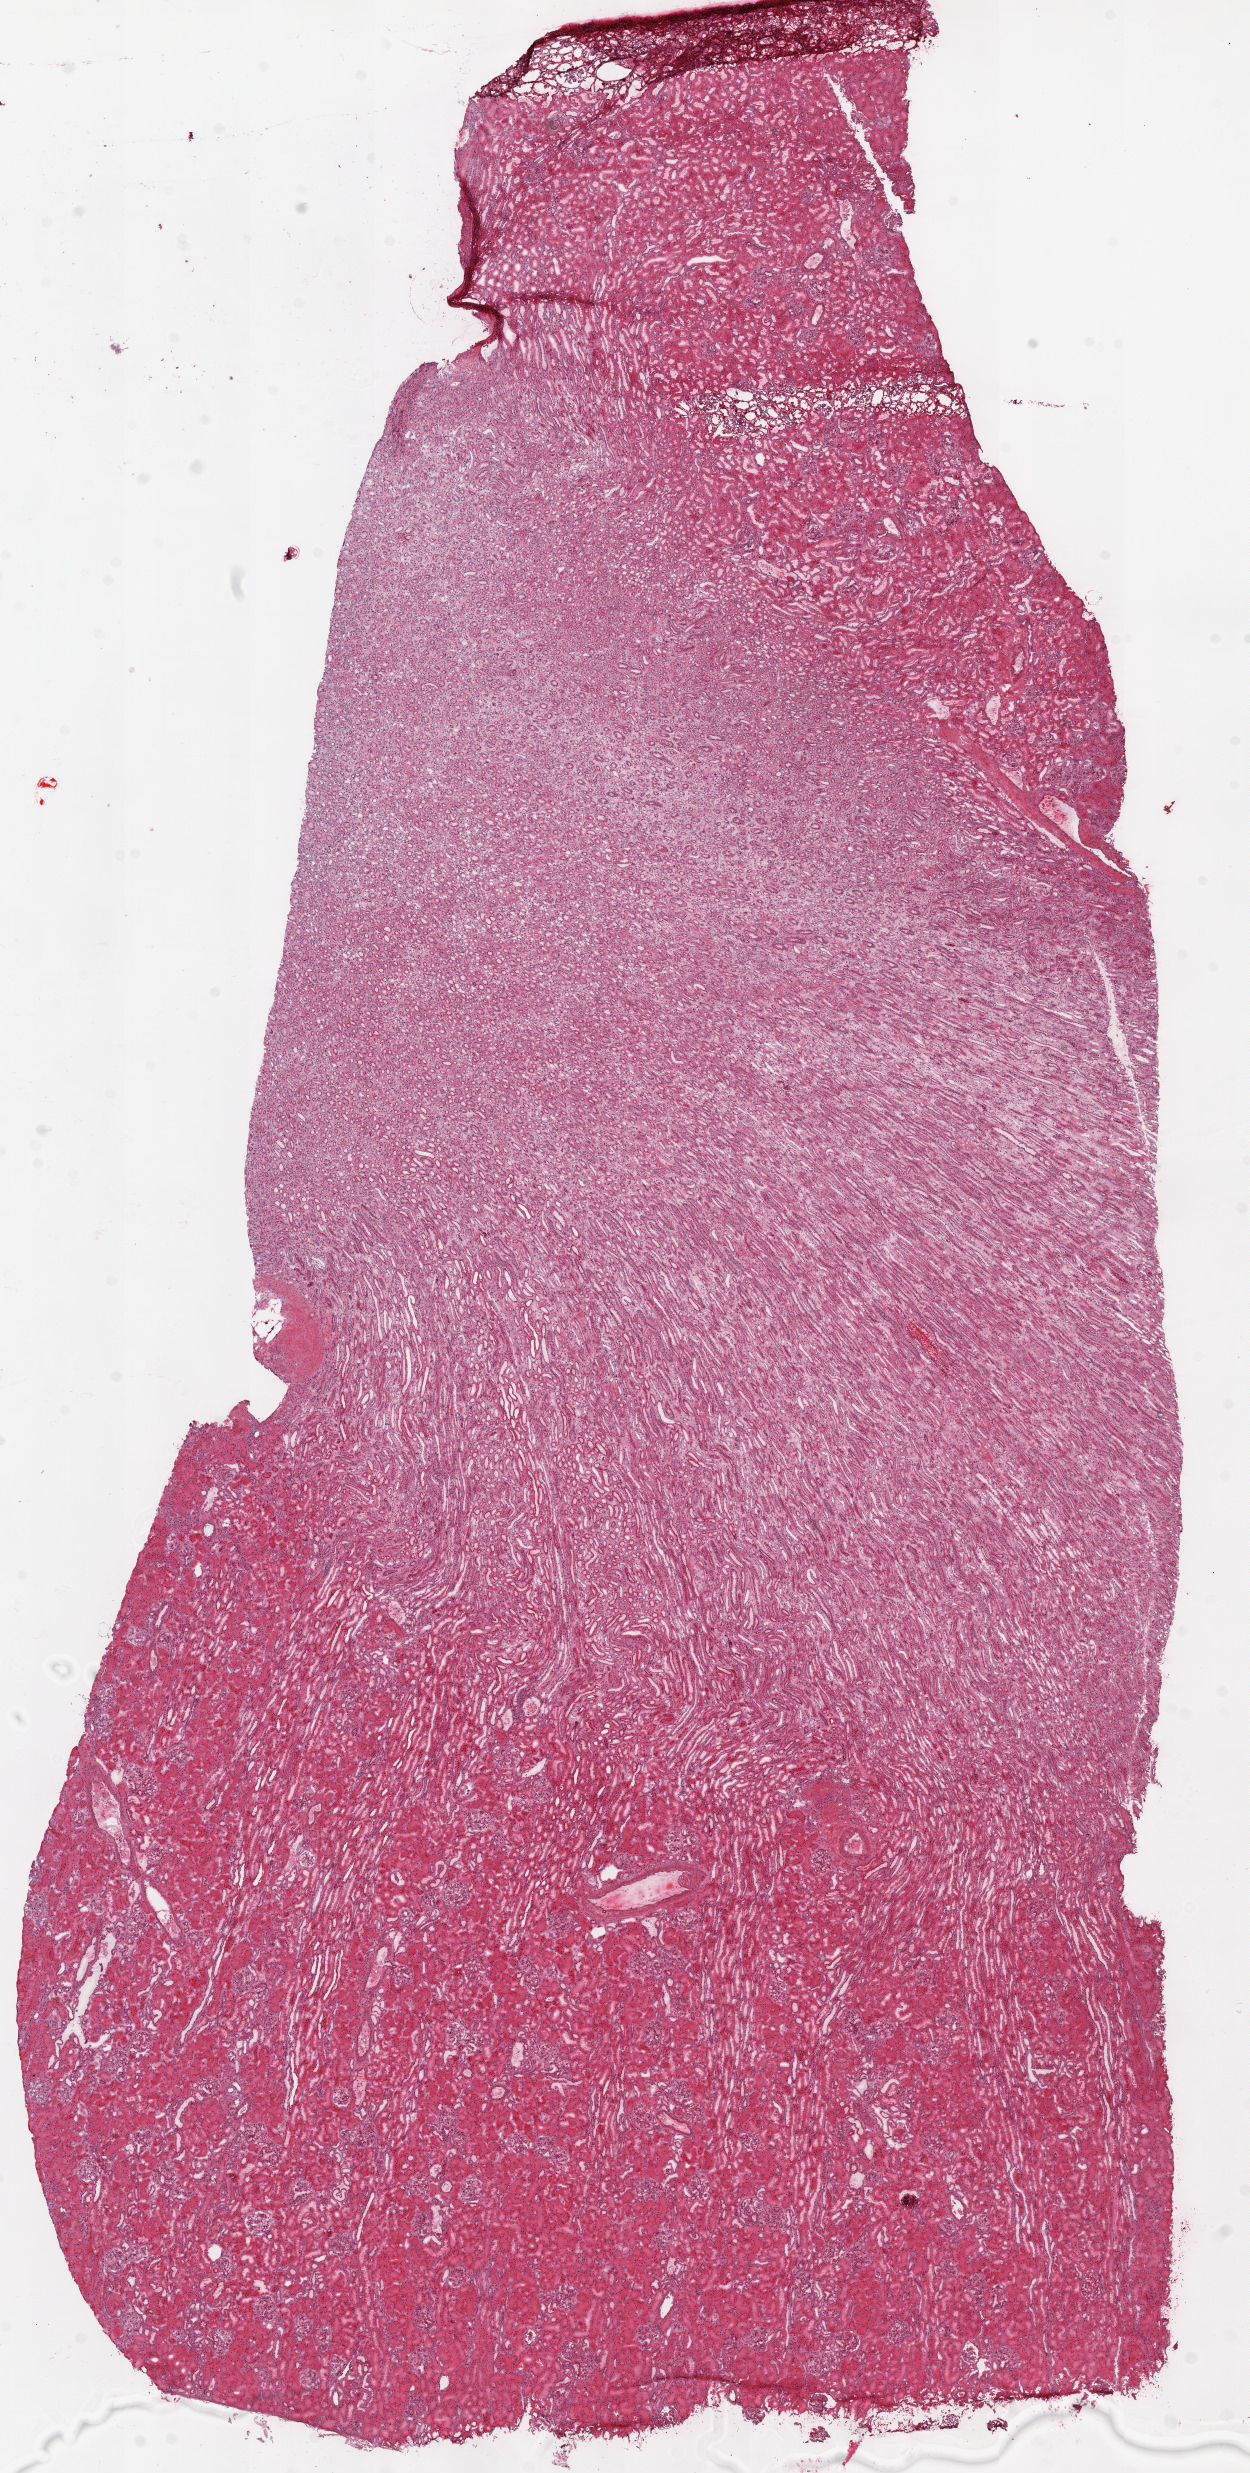
Whole-slide histology image, H&E, whole scanned area (about 10.0 x 19.8 mm) shown as a low-resolution overview; frozen section from the top of the tissue portion; kidney, solid tissue normal (non-tumour tissue) sample. Male patient; age at initial diagnosis 34 years.
This section: solid tissue normal sample (biorepository sample class). Patient diagnosis: Clear cell adenocarcinoma, NOS.